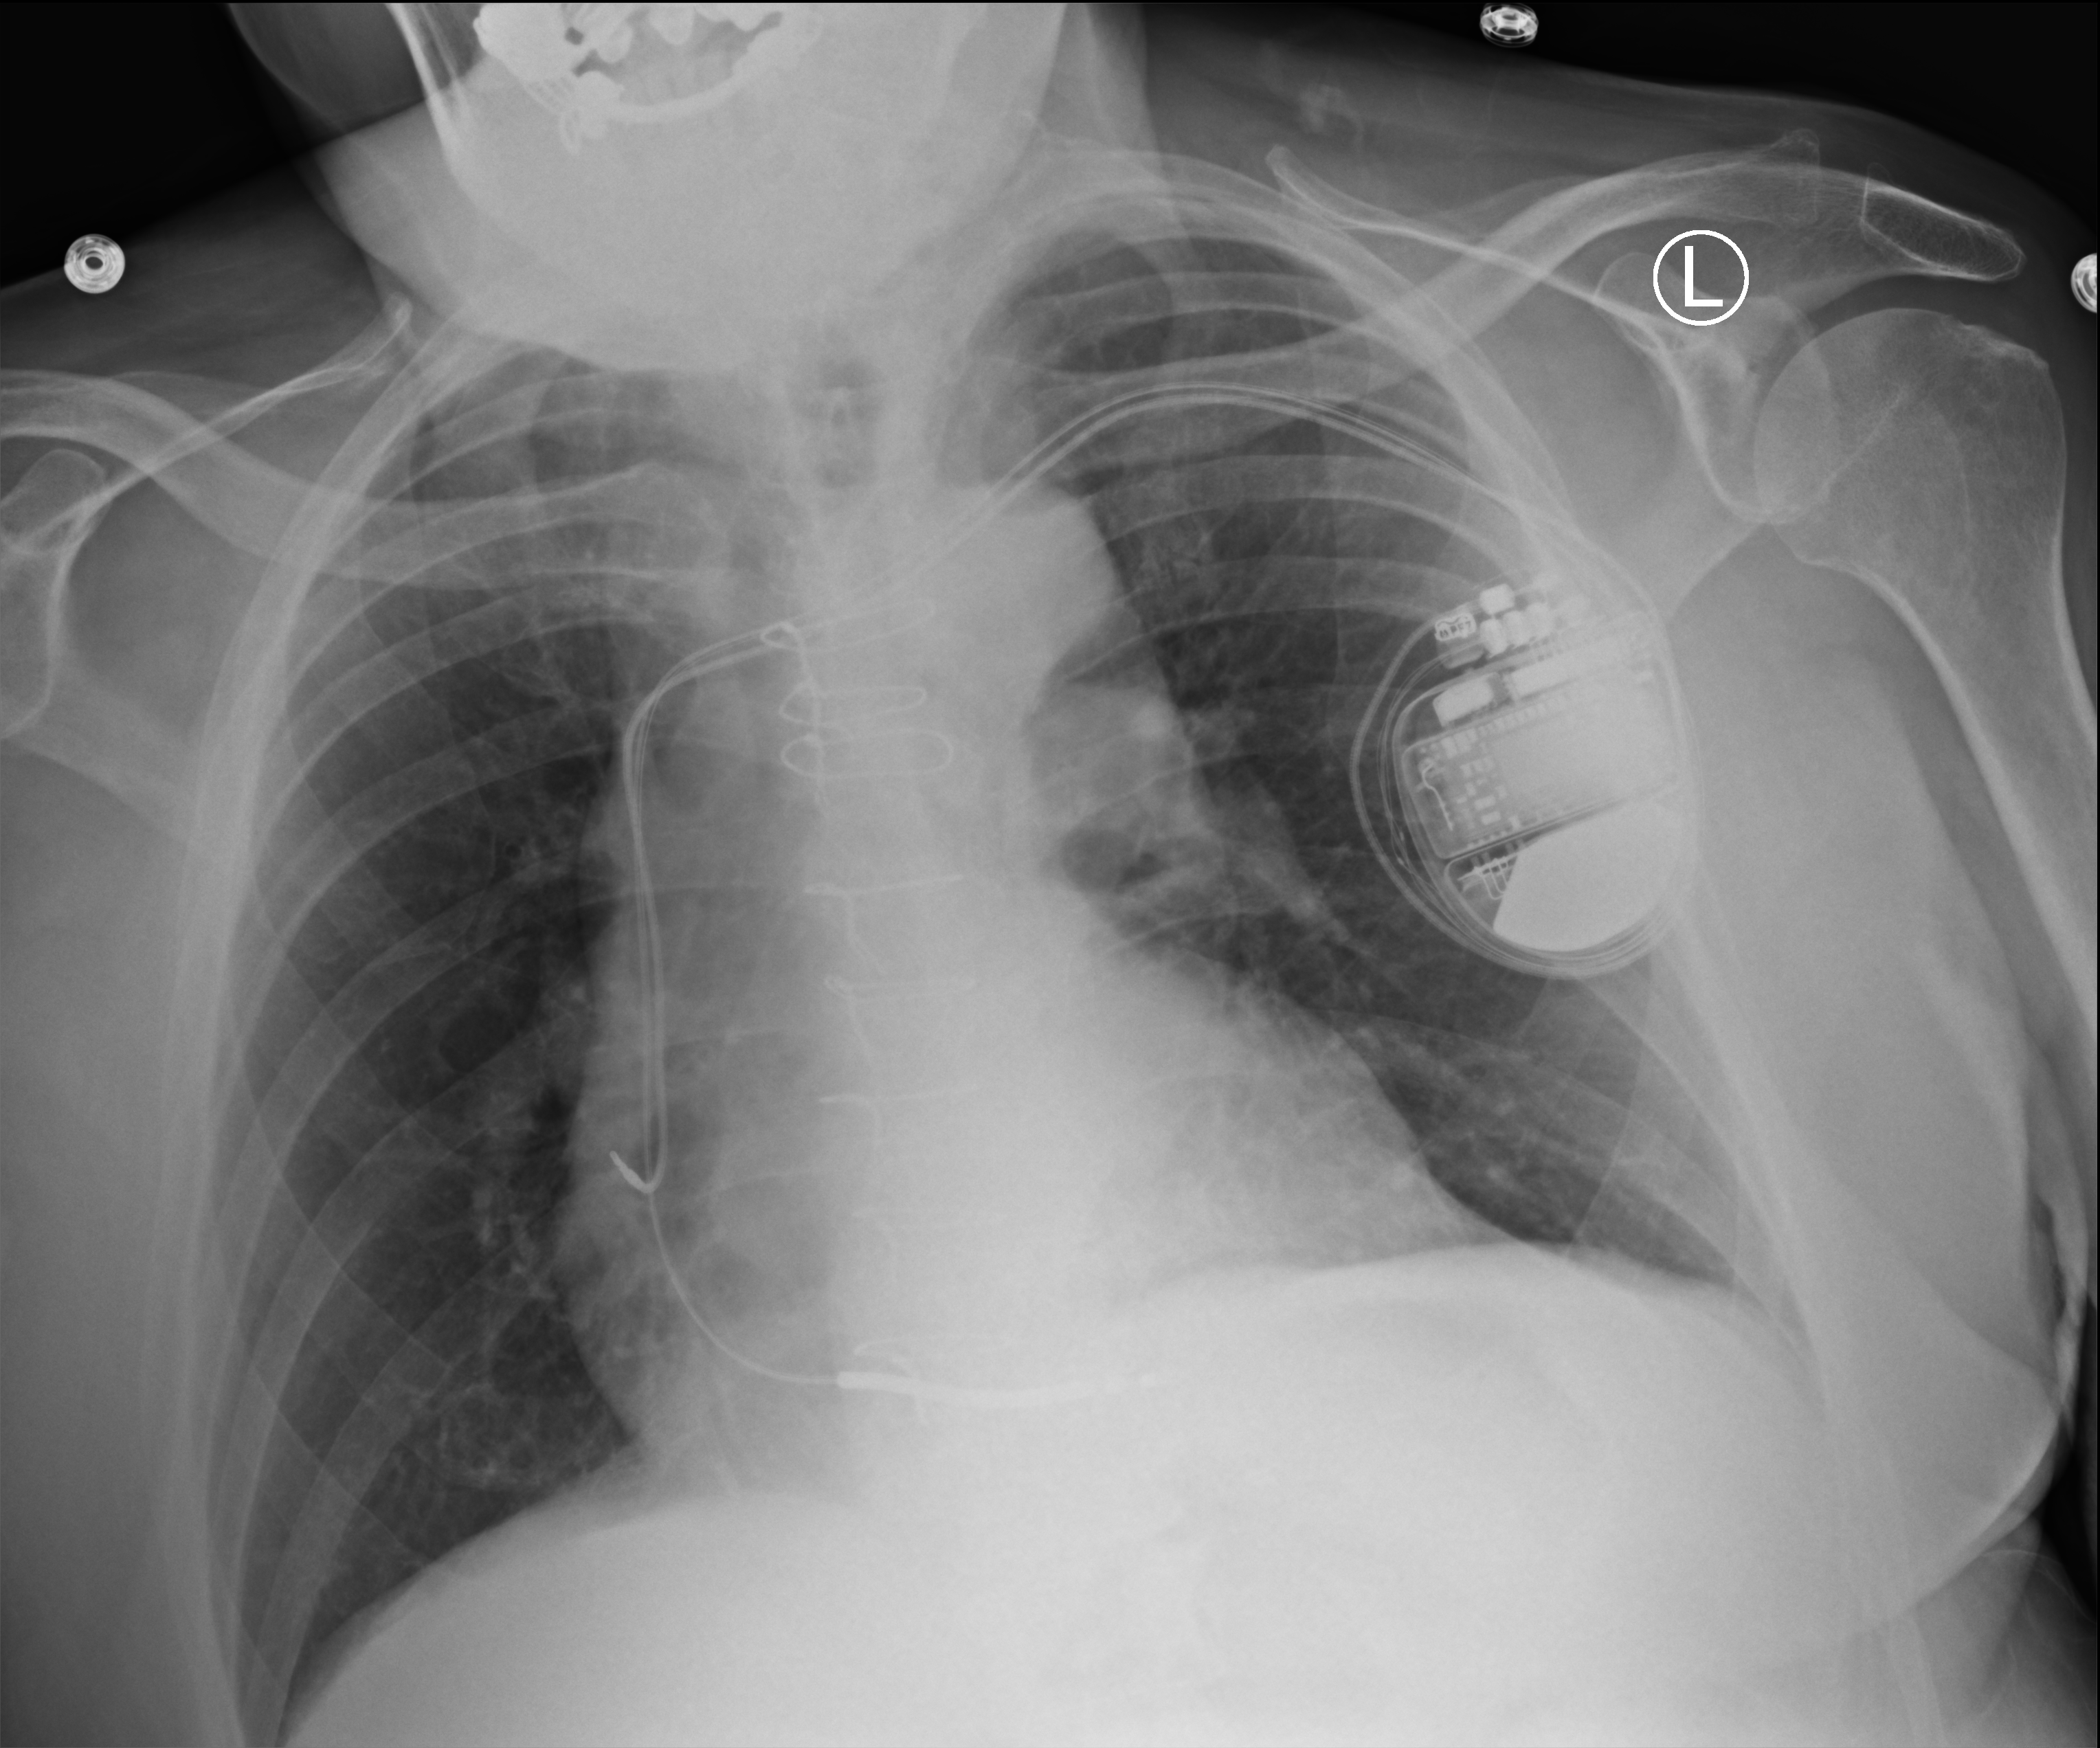
Chest X-ray (portable). Patient hospitalised with COVID-19; male, aged 75–90 years.
Hospital-stay facts (about this admission, not read from this image; timing relative to this image not recorded):
- mechanically ventilated during this hospital stay: yes